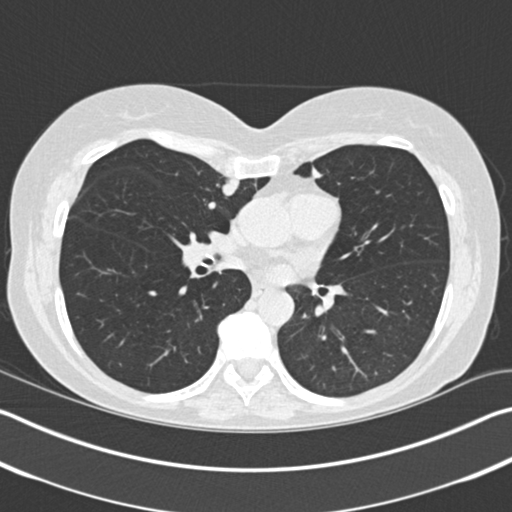
Axial slice from a low-dose chest CT screening exam; baseline screening round; lung window (W 1500 / L -600 HU); 2 mm slice thickness; standard (soft-tissue) reconstruction kernel (B30f); 120 kVp; 512 × 512 image matrix, field of view 340 × 340 mm. Female, age 61 years at enrolment. Former smoker at enrolment.
Lesion marked by an expert reader, bounding box (x1, y1, x2, y2) in pixels: (200, 169, 249, 212). The screening reader recorded 2 non-calcified nodules or masses ≥4 mm on this exam; which of them this box marks is not recorded. Participant outcome: lung cancer diagnosed 131 days after this screen — adenocarcinoma, NOS, right upper lobe, stage IA (AJCC 6th edition), 11 mm at pathology.